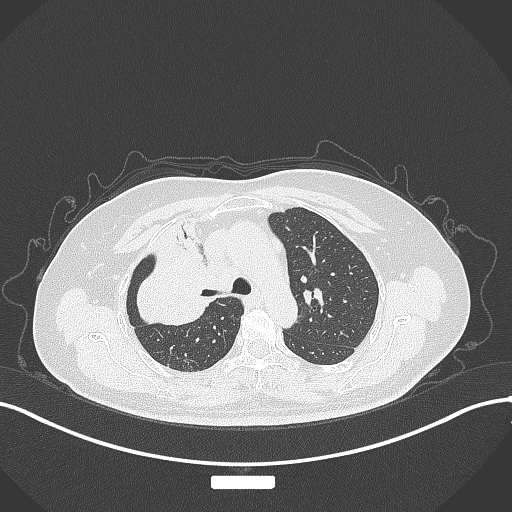
Chest CT, one axial slice; slice 220 of 309 in the series (ordered by position); reconstruction kernel B70f; lung window (W 1500 / L -600 HU); 1 mm slice thickness; 512 × 512 image matrix, field of view 400 × 400 mm. Female patient, age 60 years. Case-level facts recorded for this patient, not image findings: clinical TNM (as recorded): T3 N1 M1.
Outlined on this slice (bounding box drawn by a radiologist):
- lung tumour (recorded histology: adenocarcinoma): bounding box (x1, y1, x2, y2) in pixels: (129, 233, 226, 334)